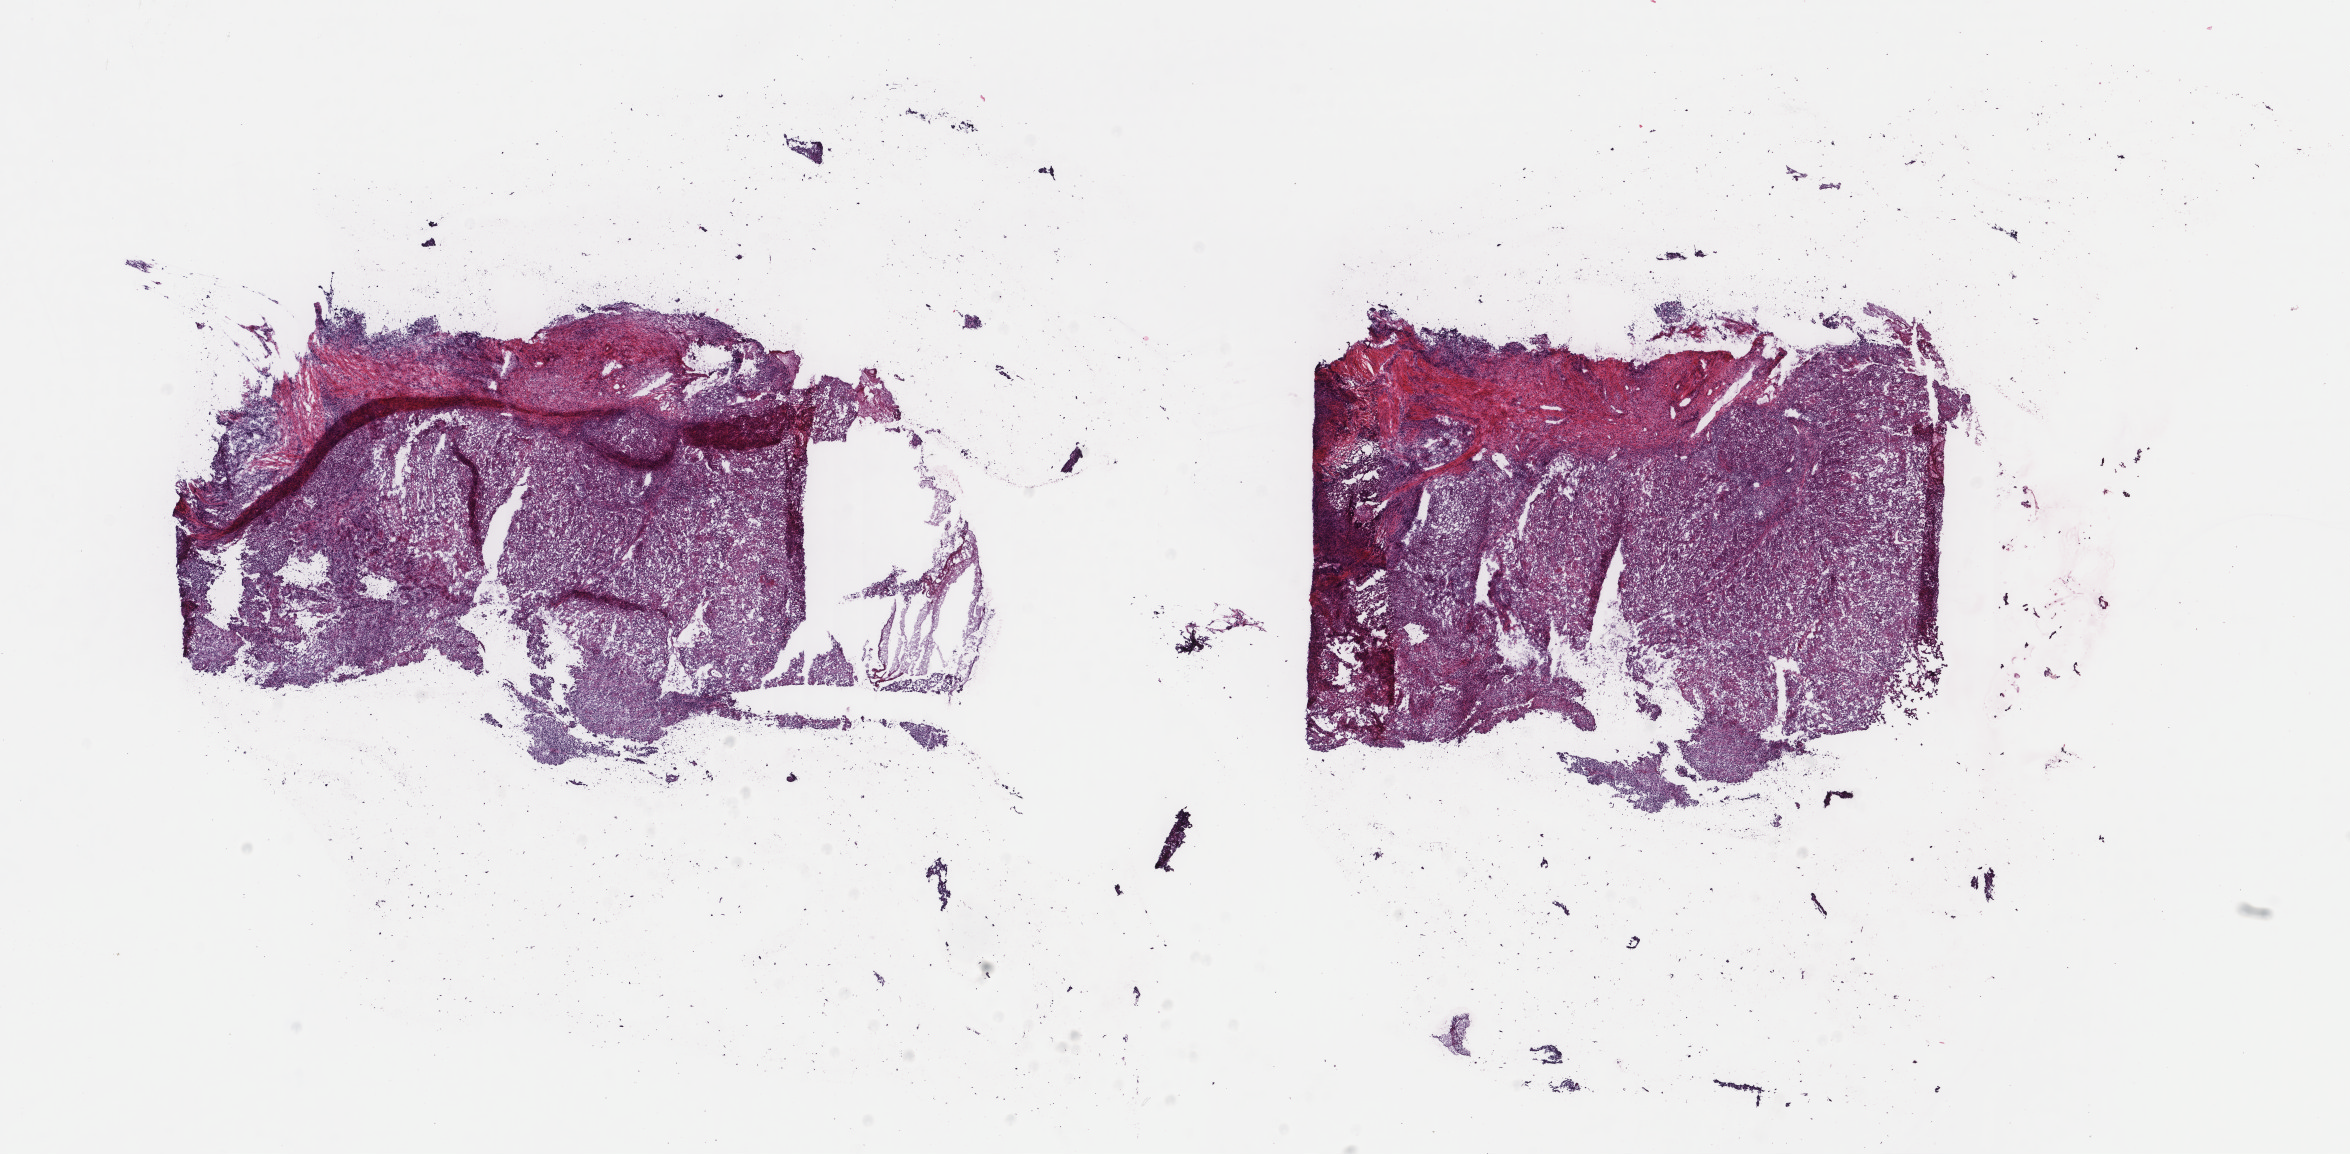
Whole-slide histology image, H&E-stained, low-resolution overview of the scanned area, about 18.7 x 9.2 mm; frozen section; cervix, primary tumour sample. Female, age 32 years at initial diagnosis. Histologic grade: G2 (moderately differentiated). Slide review estimates, as recorded: tumour cells 70%, tumour nuclei 70%, normal cells 0%, stromal cells 20%, necrosis 10%. Infiltration values recorded for this section: lymphocyte infiltration 60%, monocyte infiltration 20%, neutrophil infiltration 20%.
• FIGO stage: IB
• histologic diagnosis: Squamous cell carcinoma, NOS (cervix uteri)